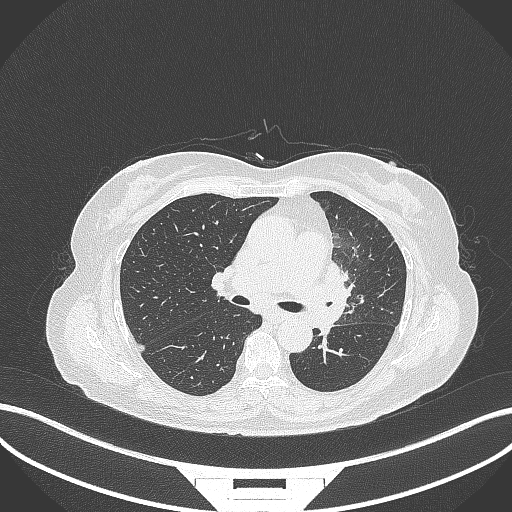
Chest CT, one axial slice; position 198 of 382 along the scan axis; reconstruction kernel B70f; 120 kVp; lung window (W 1500 / L -600 HU); 512 × 512 image matrix, field of view 400 × 400 mm. Female patient, age 64 years. From the clinical record (not read from this slice): clinical TNM (as recorded): T2a N2 M0.
Structures marked on this image (rectangle marked by the reading radiologist):
- lung tumour (recorded histology: adenocarcinoma): box from (x=319, y=256) to (x=358, y=334) px